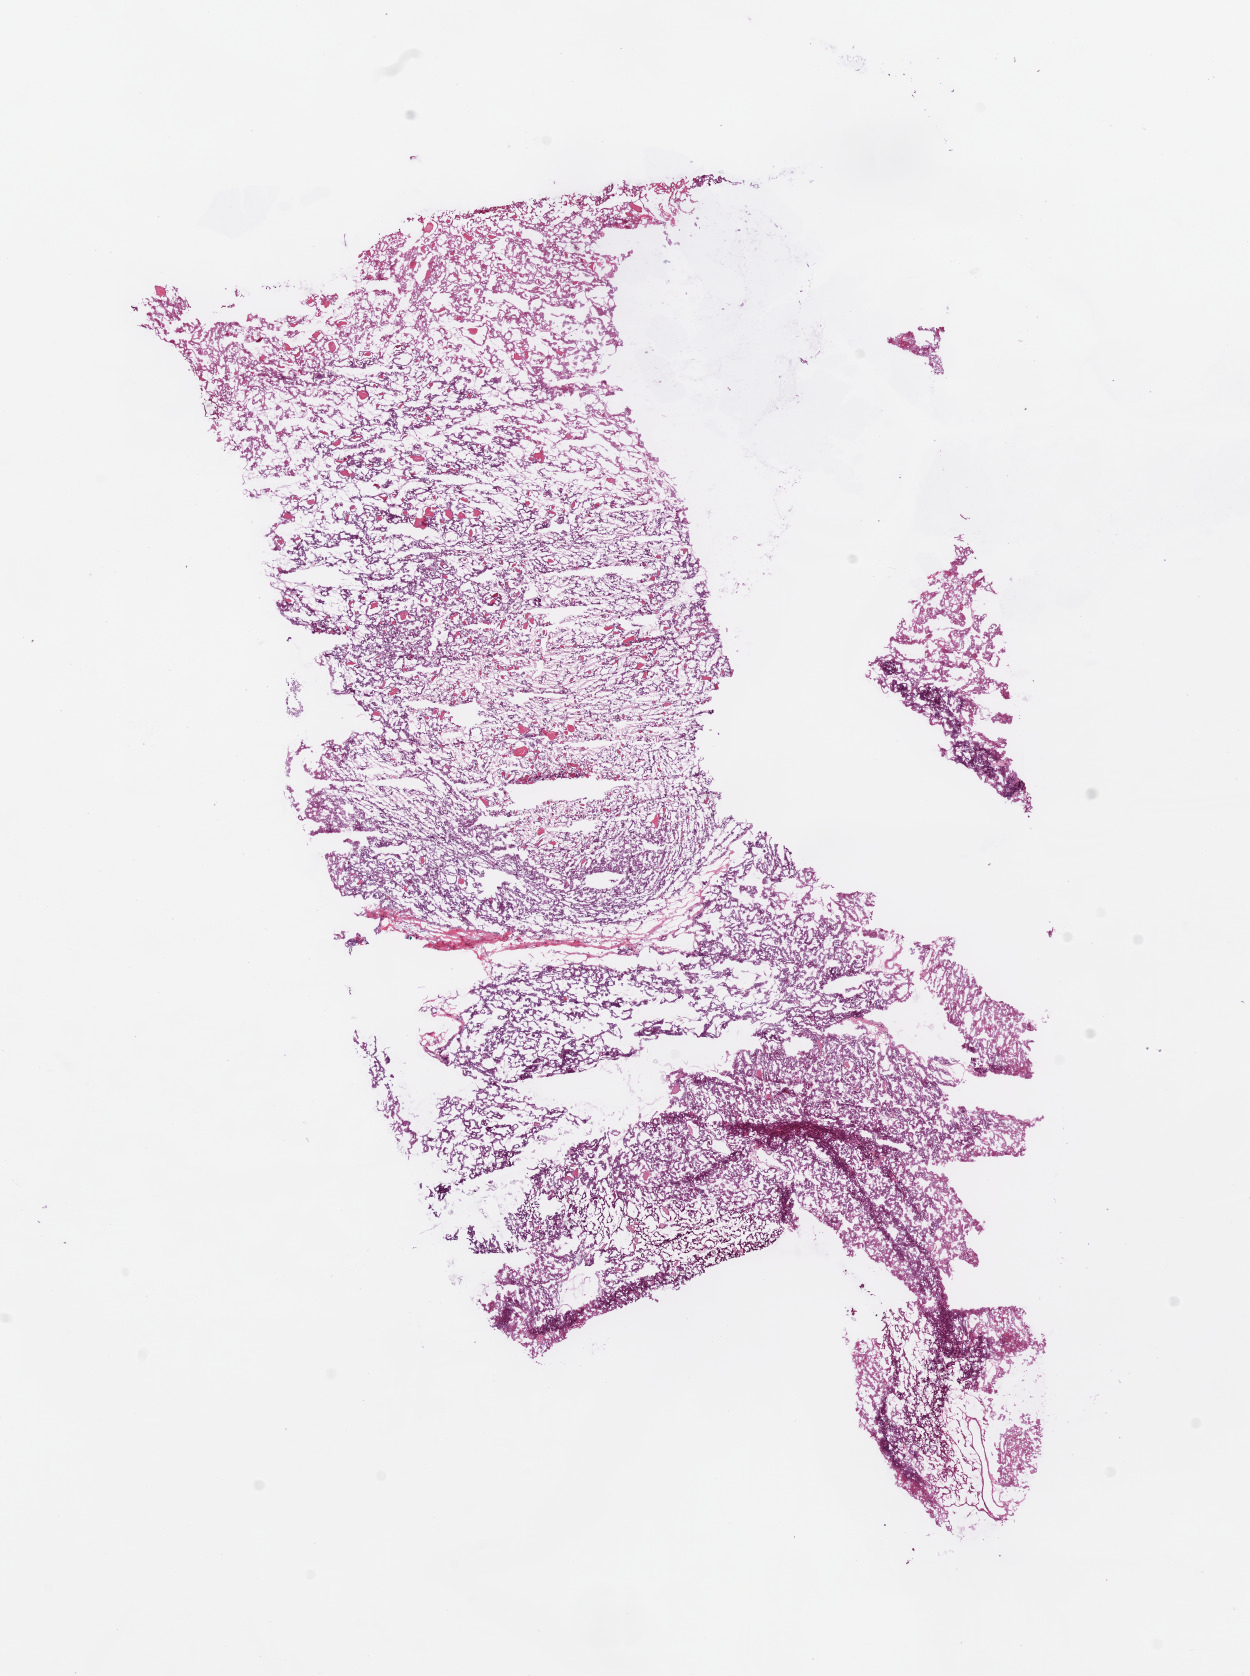
Digitized H&E-stained tissue section (whole slide) — low-resolution overview of the scanned area, about 10.0 x 13.4 mm (acquisition: 20x scan), frozen section, sample: primary tumour, kidney. Female, age 58 years at initial diagnosis. Histologic grade: G2 (moderately differentiated). Pathologist review of this section (percent, as recorded): tumour cells 95%, tumour nuclei 85%, normal cells 0%, stromal cells 5%, necrosis 0%.
Pathologic diagnosis: Clear cell adenocarcinoma, NOS. AJCC pathologic stage: II (6th edition).